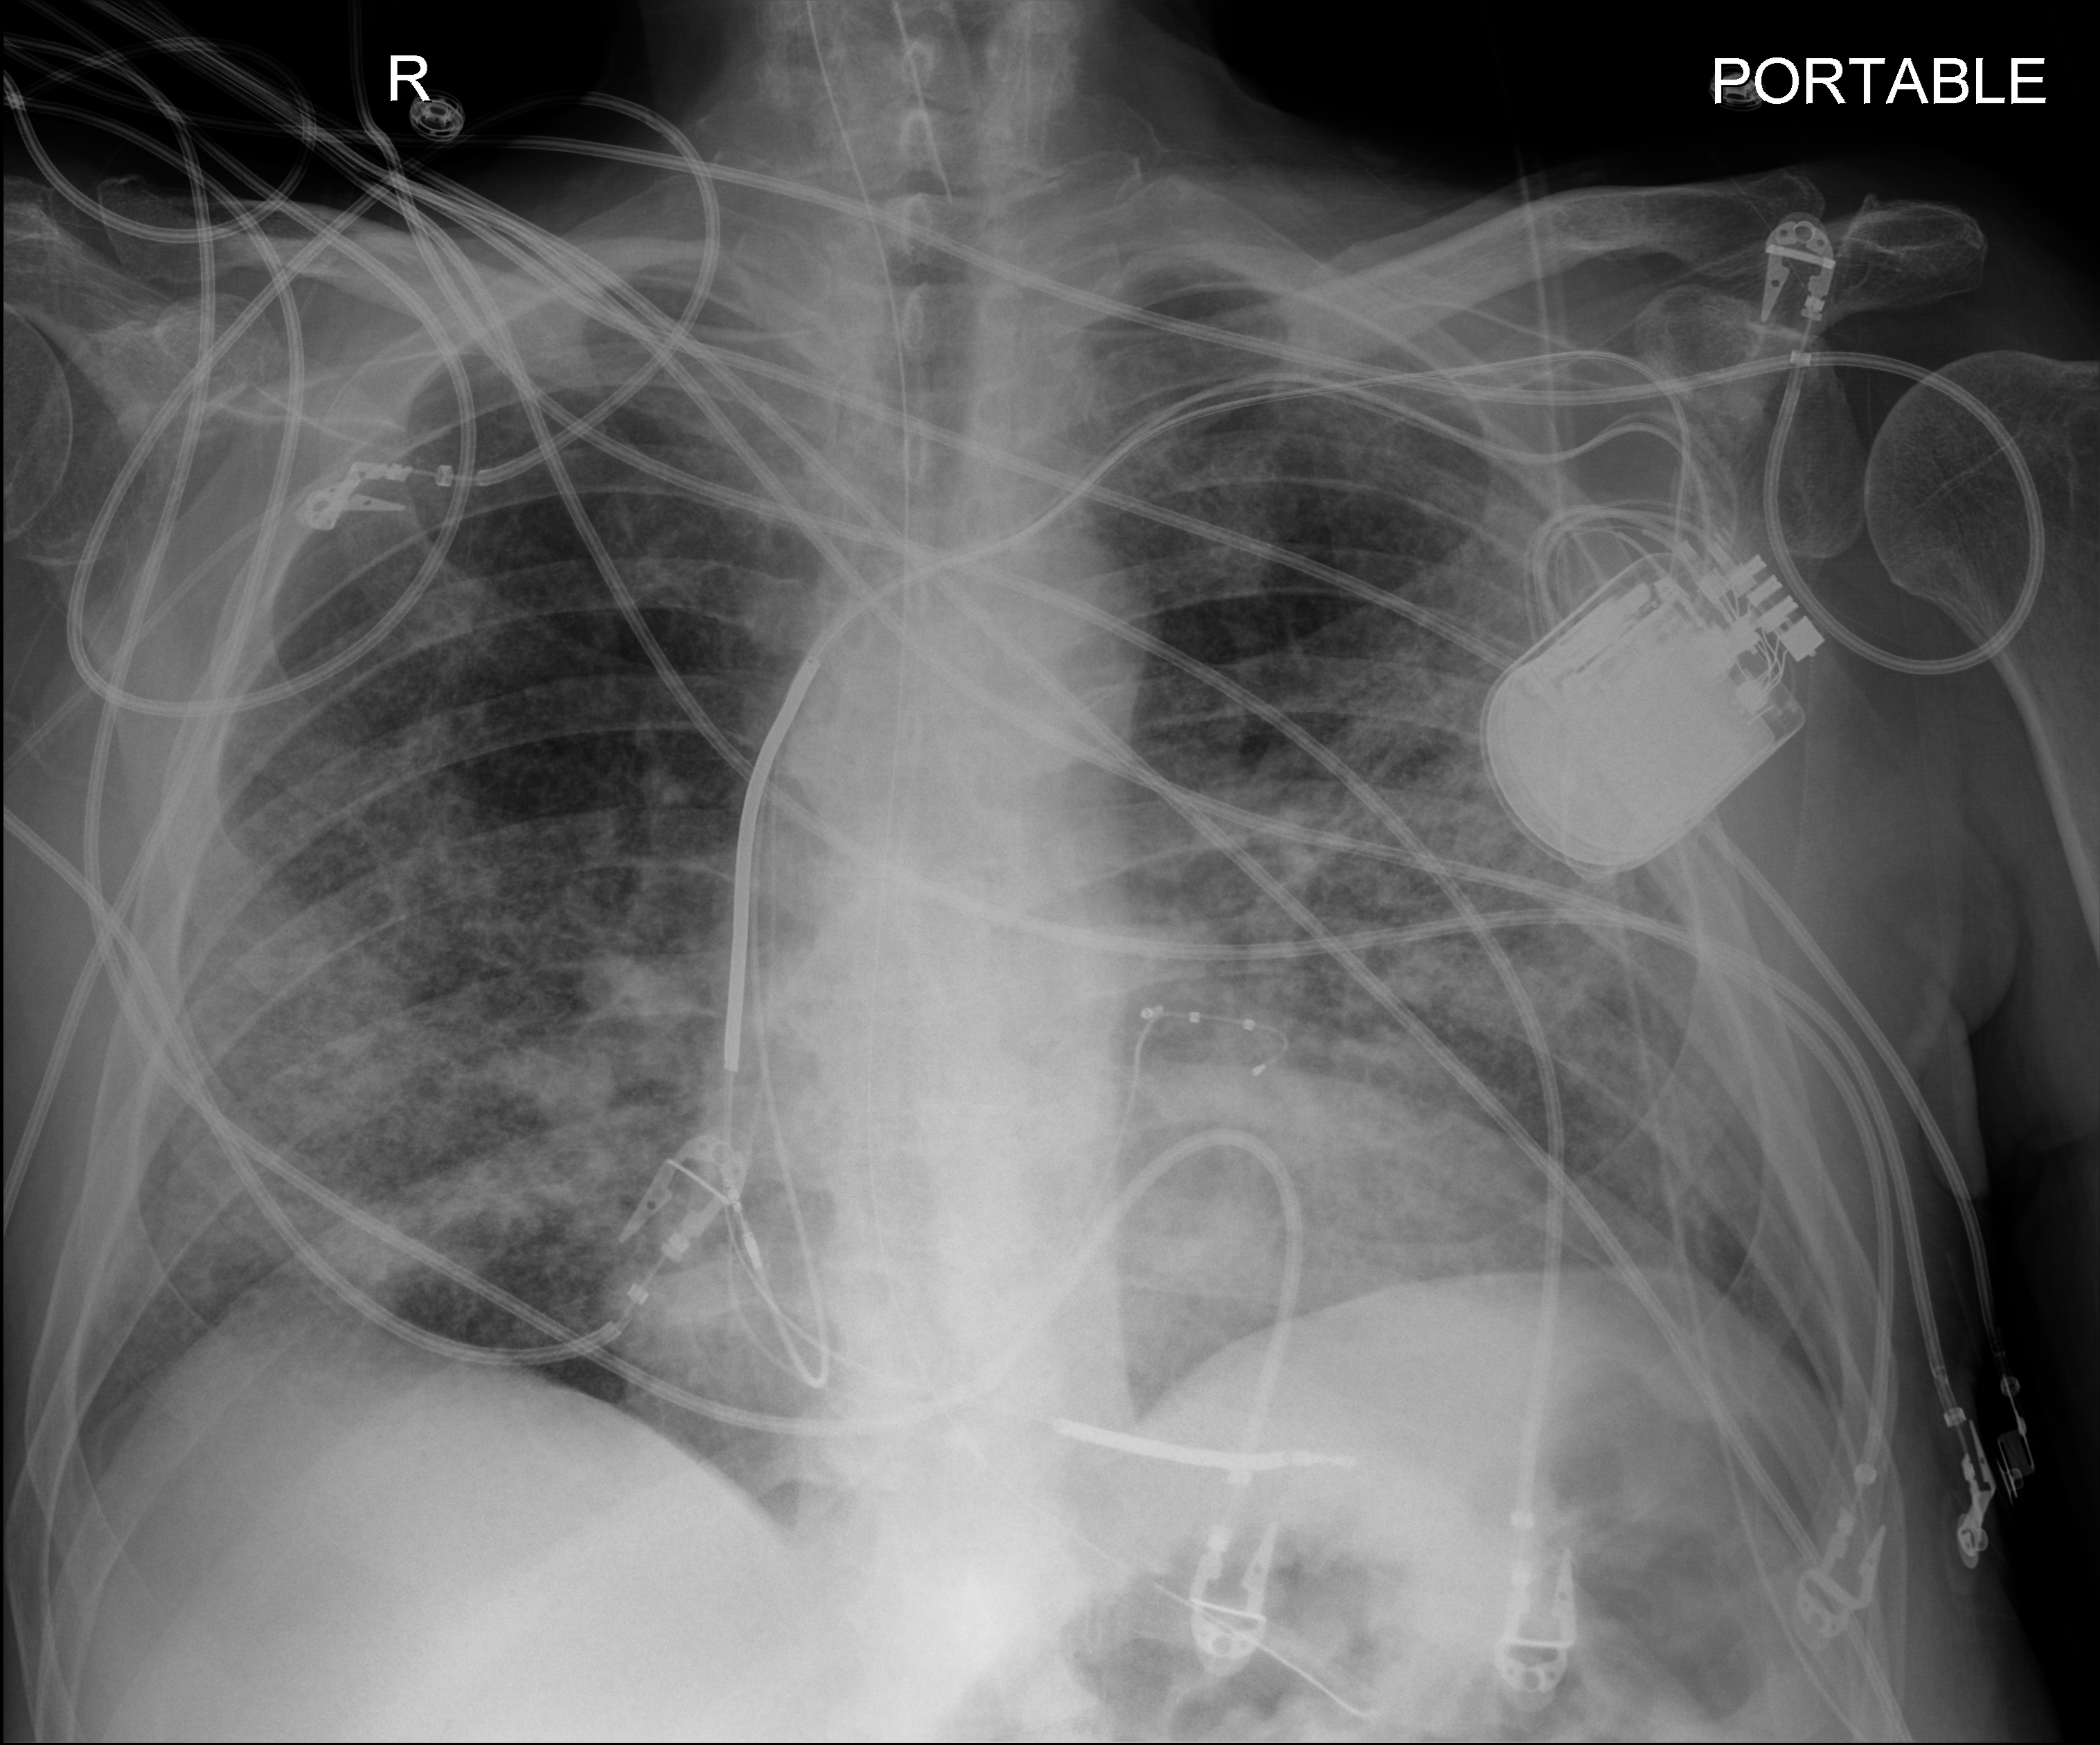
Portable chest radiograph, anteroposterior (AP) projection. Patient hospitalised with COVID-19; male, aged 60–74 years.
Hospital-stay facts (about this admission, not read from this image; timing relative to this image not recorded): admitted to intensive care during this hospital stay: yes.